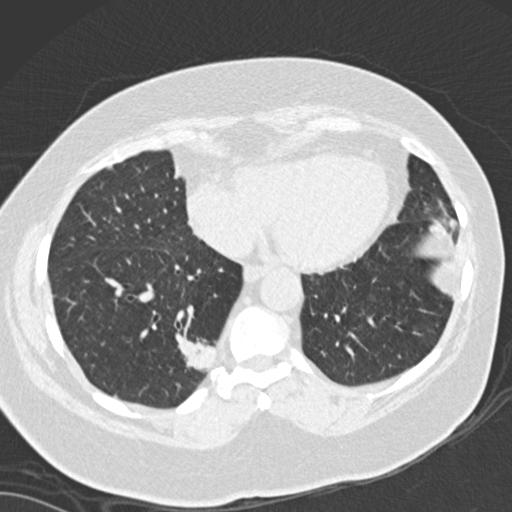
Low-dose screening chest CT, one axial slice. Slice 52 of 162 in the series (ordered by position). 120 kVp. Lung window (W 1500 / L -600 HU). 2 mm slice thickness. 512 × 512 image matrix, field of view 328 × 328 mm.
Outlined on this slice (outlined manually by an expert reader):
- lesion 1 (tumor, lower lobe of right lung): bounding box [x1, y1, x2, y2] px = [178, 339, 216, 372]